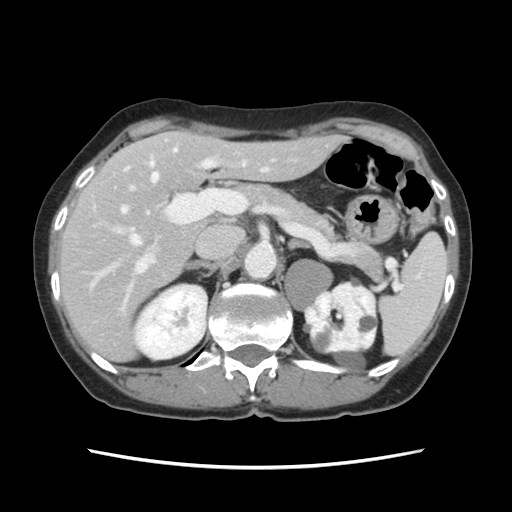
Contrast-enhanced abdominal CT, one axial slice; position 77 of 120 along the scan axis; 120 kVp; intravenous contrast given; soft-tissue window (W 400 / L 40 HU); 2.5 mm slice thickness; 512 × 512 image matrix, field of view 330 × 330 mm. Female patient, age 70 years. From the clinical record (not read from this slice): diagnosis: colorectal cancer liver metastases, imaged before liver resection; multiple liver metastases: no; largest metastasis: 2.5 cm.
Annotated regions visible in this slice (outlined manually by an expert reader):
- hepatic veins: bounding box (x1, y1, x2, y2) in pixels: (109, 149, 177, 270)
- liver: (60, 132, 339, 360)
- planned liver remnant (the part of the liver to remain after resection): (94, 132, 340, 285)
- portal vein (with intrahepatic branches): (121, 140, 246, 308)